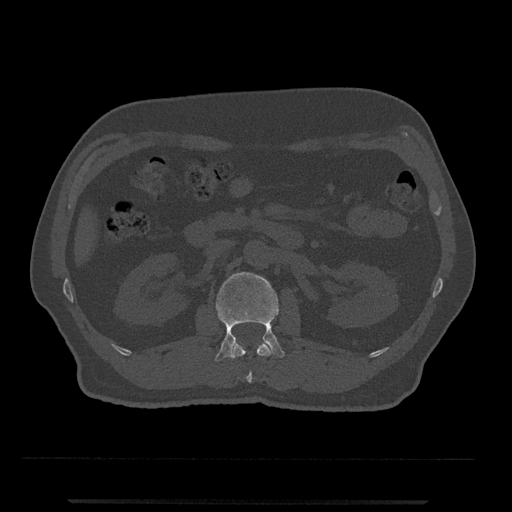
CT including the spine, one axial slice; position 292 of 797 along the scan axis; reconstruction kernel Br40s/3; 120 kVp; bone window (W 1800 / L 400 HU); 512 × 512 image matrix, field of view 419 × 419 mm. Male patient, age 63 years. From the clinical record (not read from this slice): primary cancer: prostate.
Annotated regions visible in this slice (semi-automatically segmented with operator editing):
- L1 vertebra: box from (x=230, y=342) to (x=273, y=383) px
- L2 vertebra: (x=215, y=272)–(x=285, y=361)